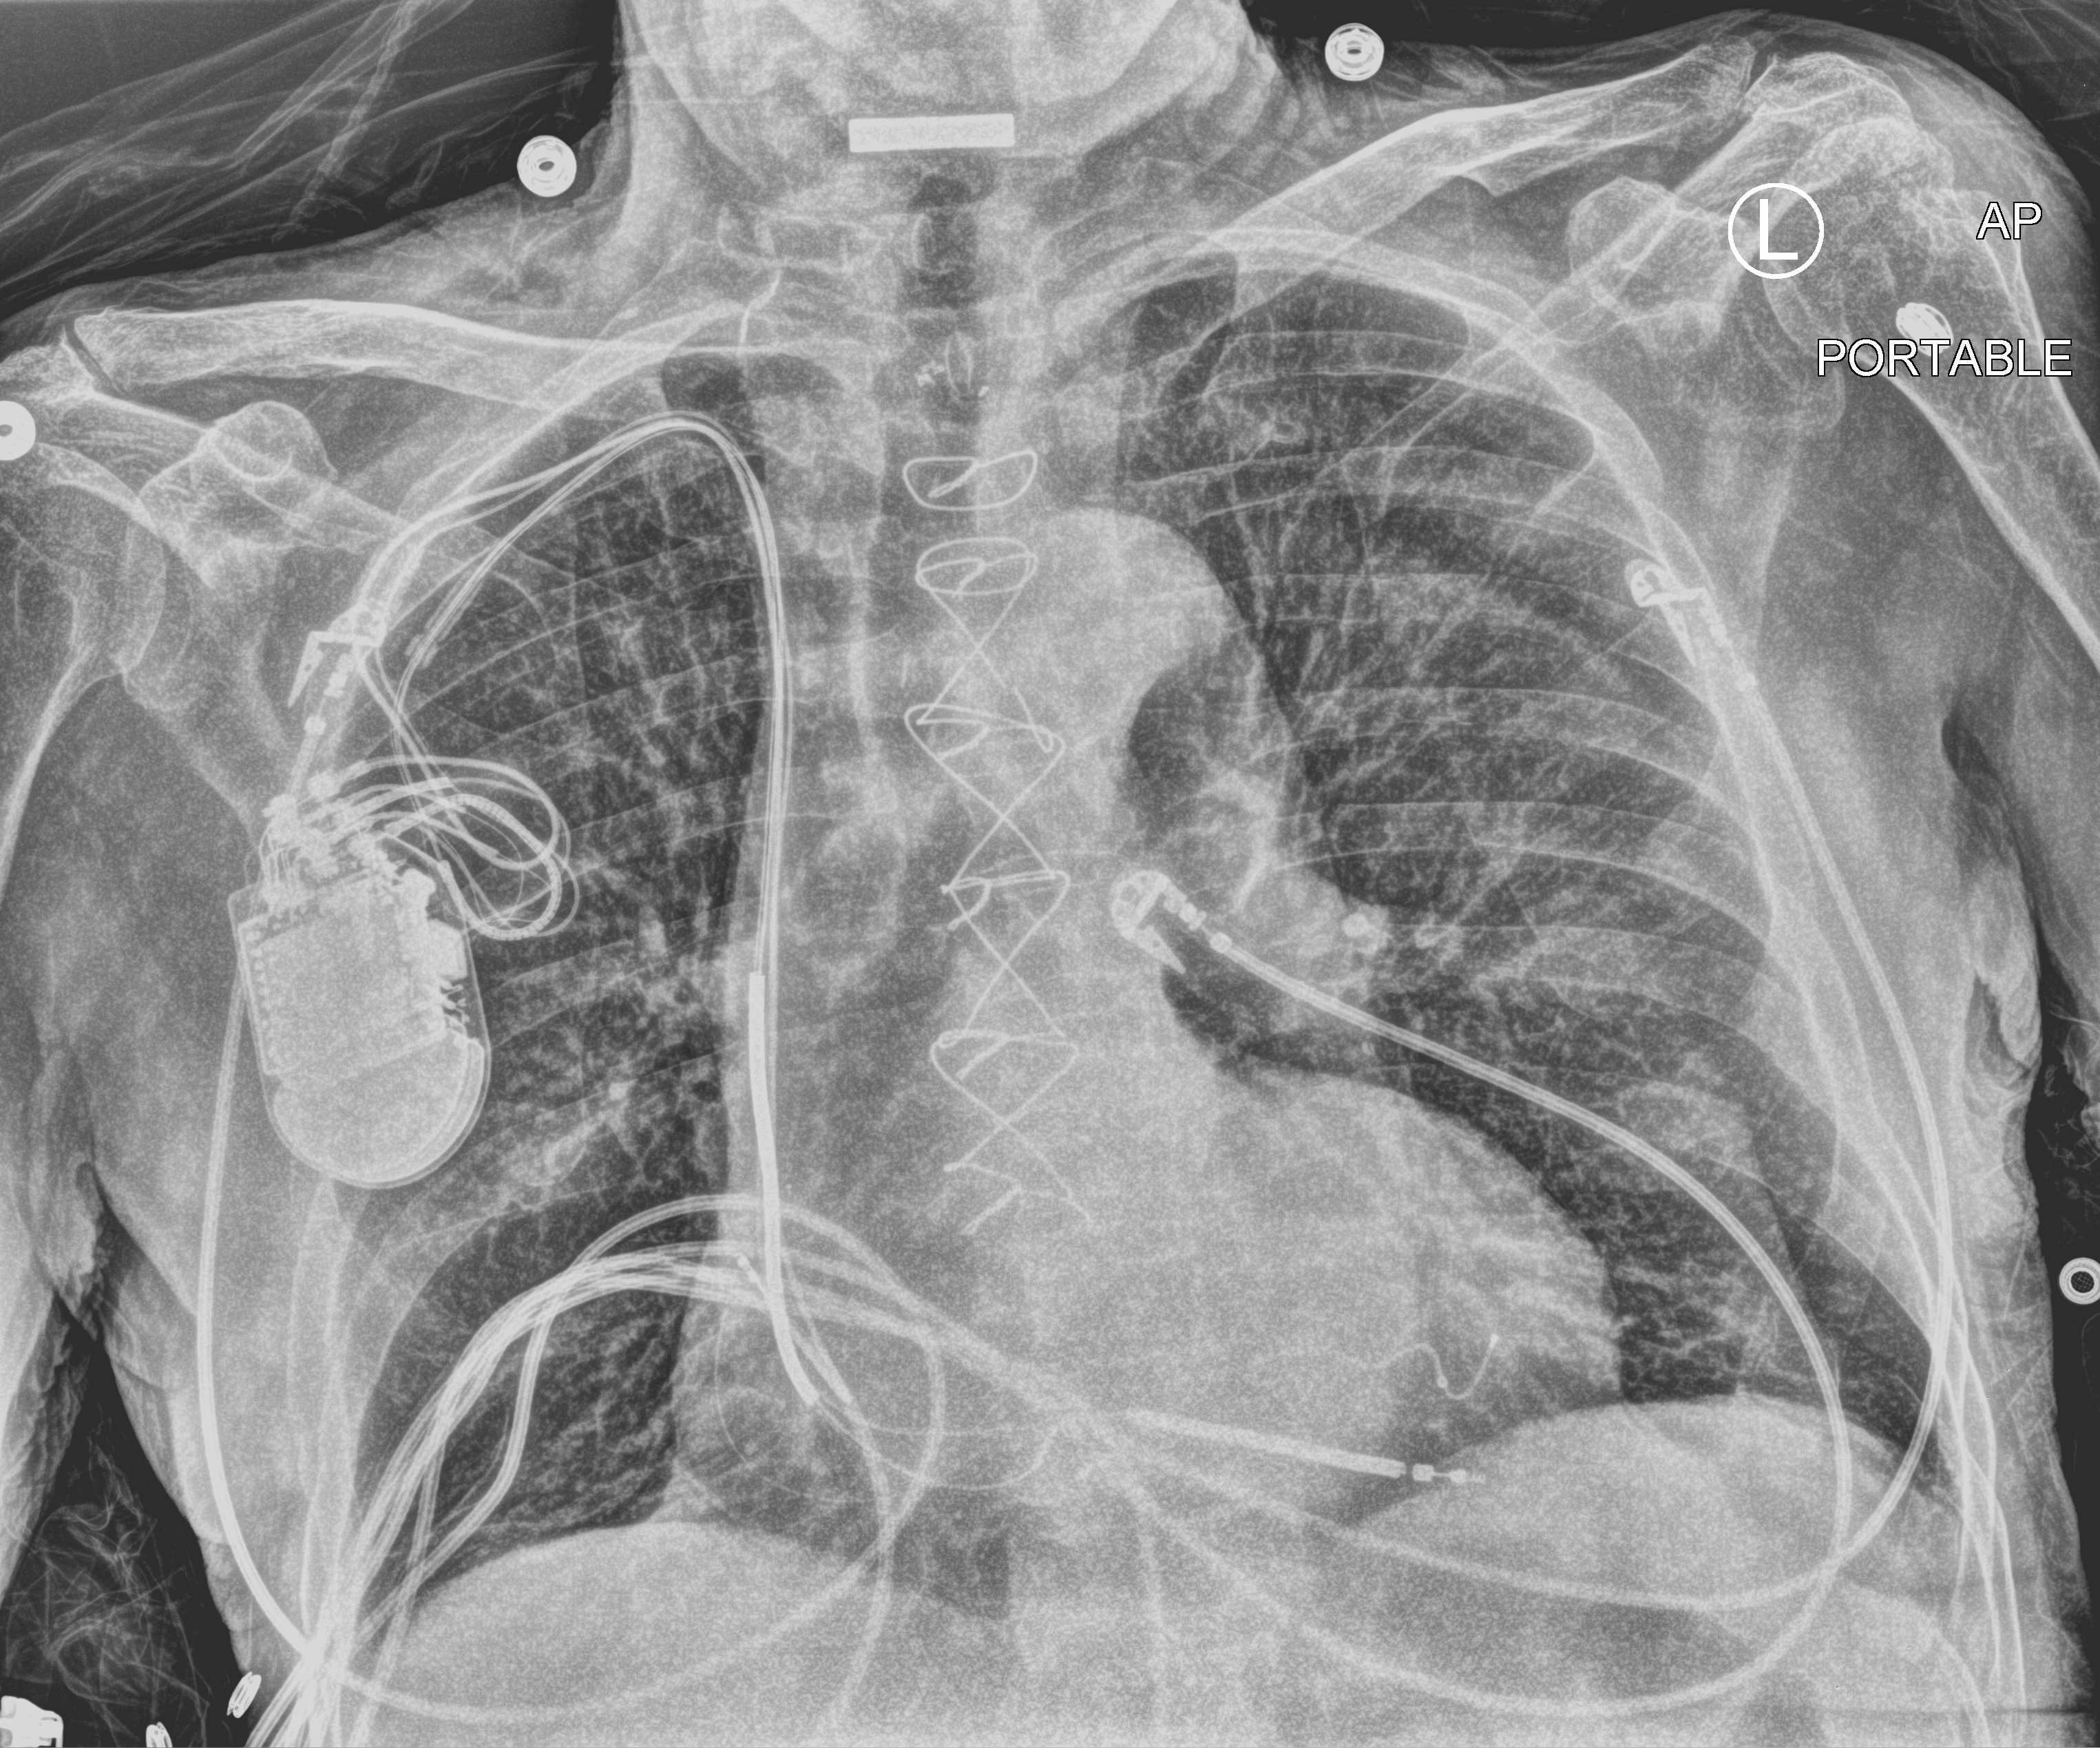
Bedside chest radiograph (computed radiography), anteroposterior (AP) projection. Patient hospitalised with COVID-19; male, aged 75–90 years.
Hospital-stay facts (about this admission, not read from this image; timing relative to this image not recorded):
- admitted to intensive care during this hospital stay: no